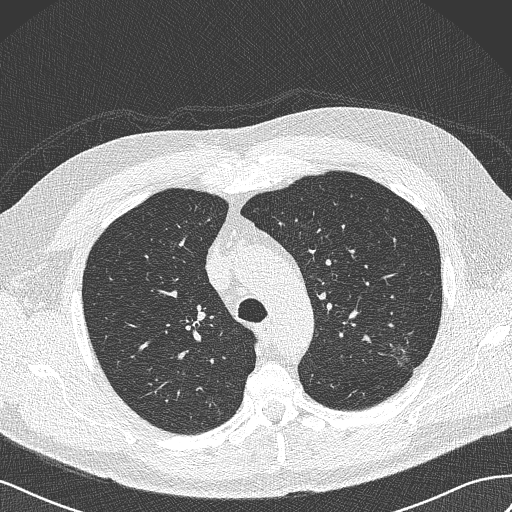
Chest CT (low-dose screening protocol), one axial image. First (baseline) screen. Lung window (W 1500 / L -600 HU). Lung (sharp) reconstruction kernel (B50f). Slice 115 of 462 in the series. Male participant, aged 65 years at enrolment. Former smoker at enrolment.
Lesion marked by an expert reader, bounding box <383,339,421,372> (left, top, right, bottom; pixels). The screening reader recorded 3 non-calcified nodules or masses ≥4 mm on this exam (left upper lobe, left upper lobe, right upper lobe); which of them this box marks is not recorded. Official screen result: positive, change unspecified: nodule(s) >= 4 mm or enlarging nodule(s), mass(es), or other non-specific abnormalities suspicious for lung cancer. Later outcome: lung cancer diagnosed 541 days after this screen (after the second annual screen) — adenocarcinoma, NOS, left upper lobe, poorly differentiated (G3), stage IA (AJCC 6th edition), 13 mm at pathology.